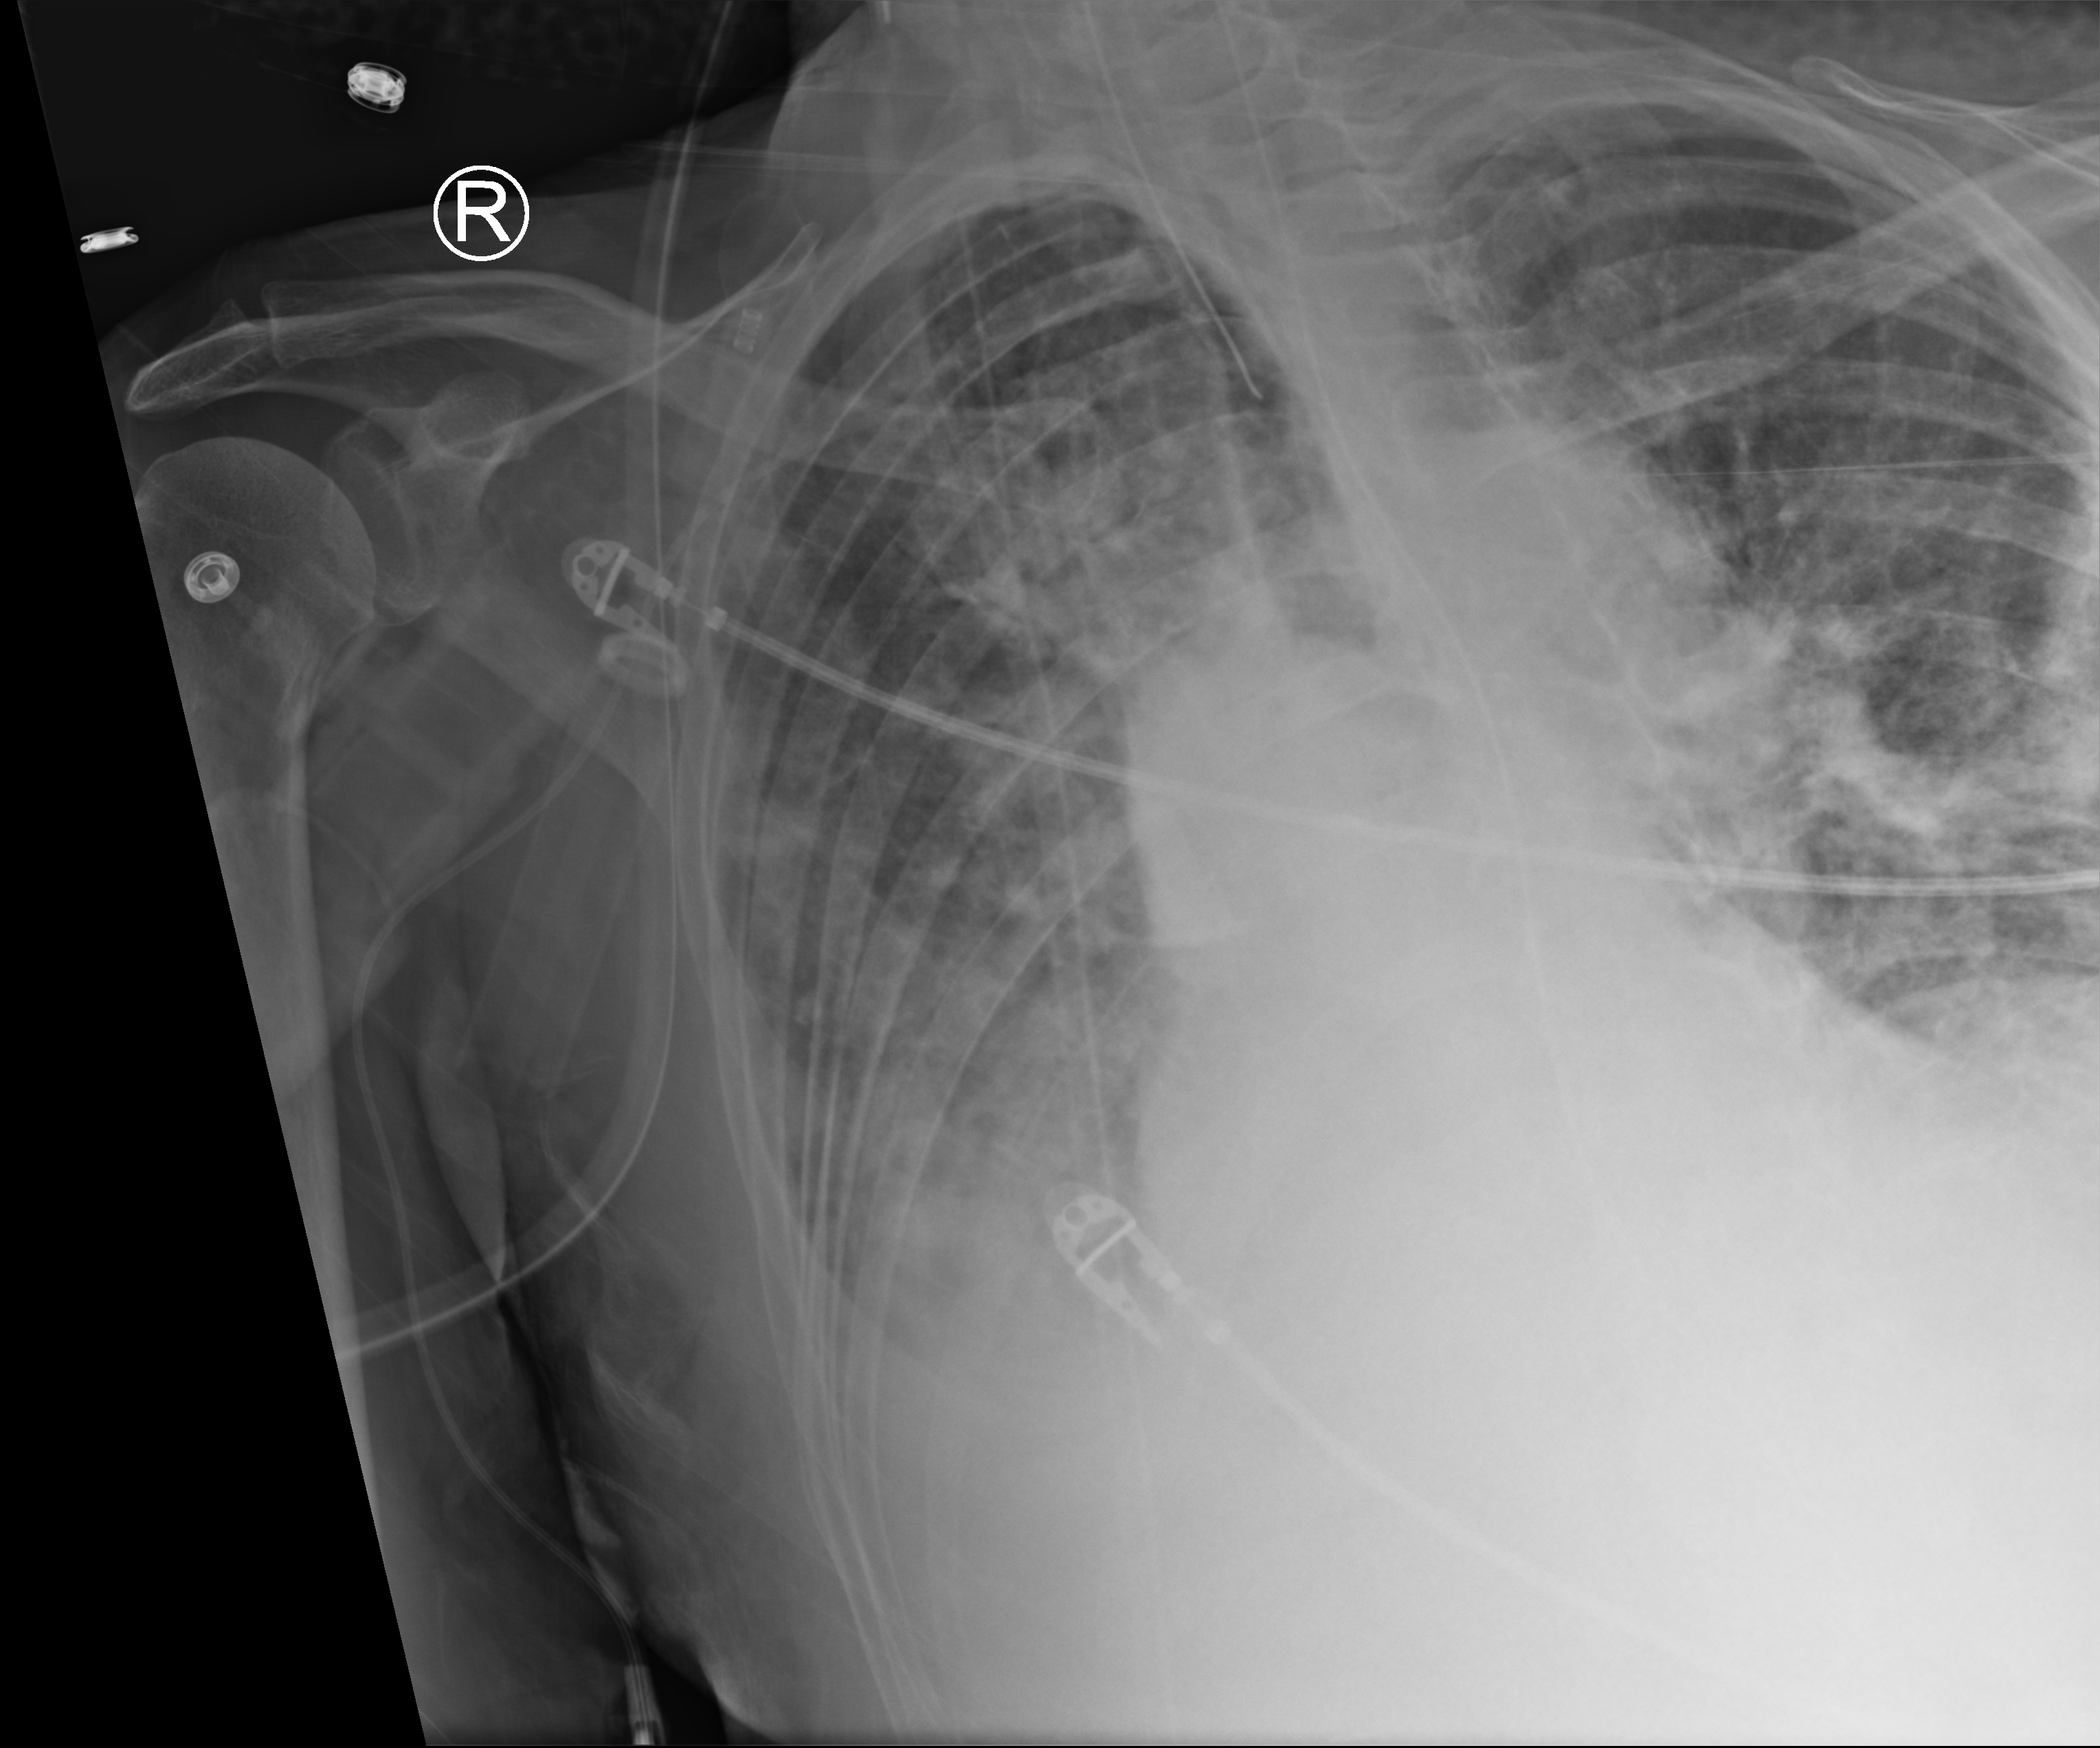
Bedside chest radiograph (computed radiography); anteroposterior (AP) projection. Patient hospitalised with COVID-19; male, aged 75–90 years.
From the hospital-stay record, not from the radiograph (when in the stay this image was taken is not recorded): diabetes (admission record): no; other chronic lung disease (admission record): yes; mechanically ventilated during this hospital stay: yes.